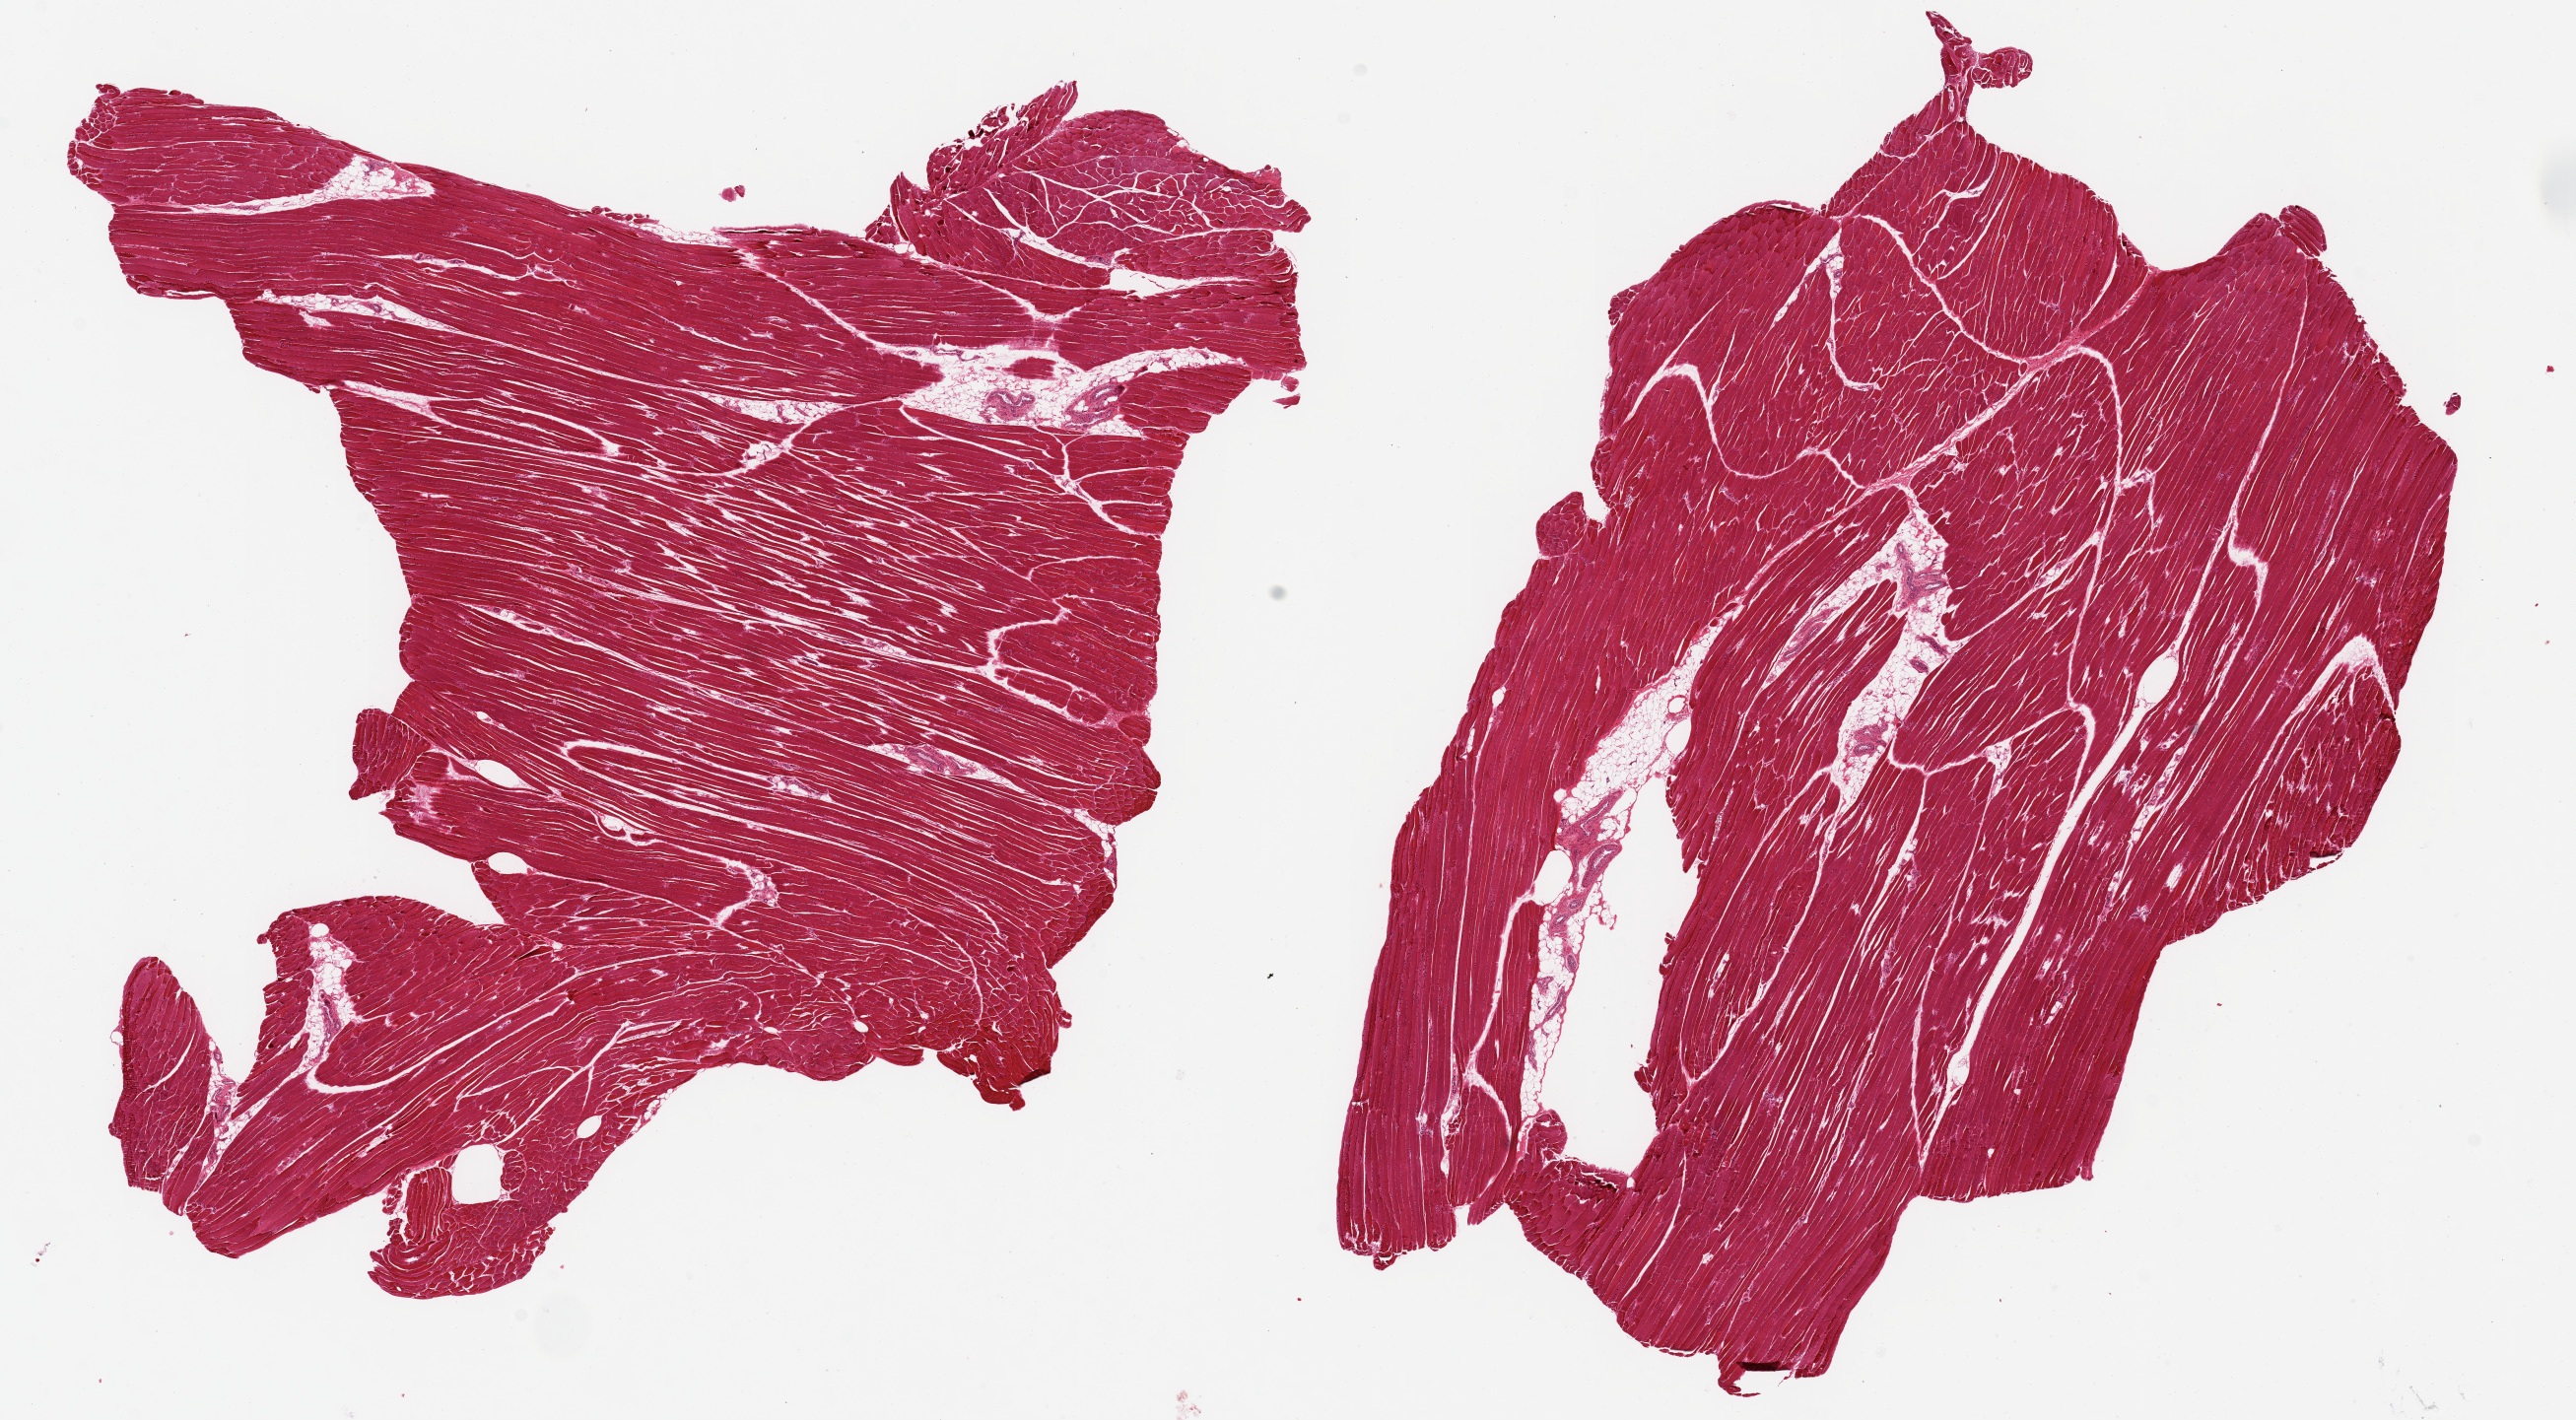
Hematoxylin and eosin (H&E) whole-slide image — low-resolution overview of the scanned area, about 20.7 x 11.4 mm, PAXgene-fixed paraffin-embedded (PFPE) section, target tissue: skeletal muscle, tissue donor sample. Donor sex: male.
Pathologist's review note for this sample: 2 pieces, 11x10 & 11x7mm; ~50-10% interstitial fat.